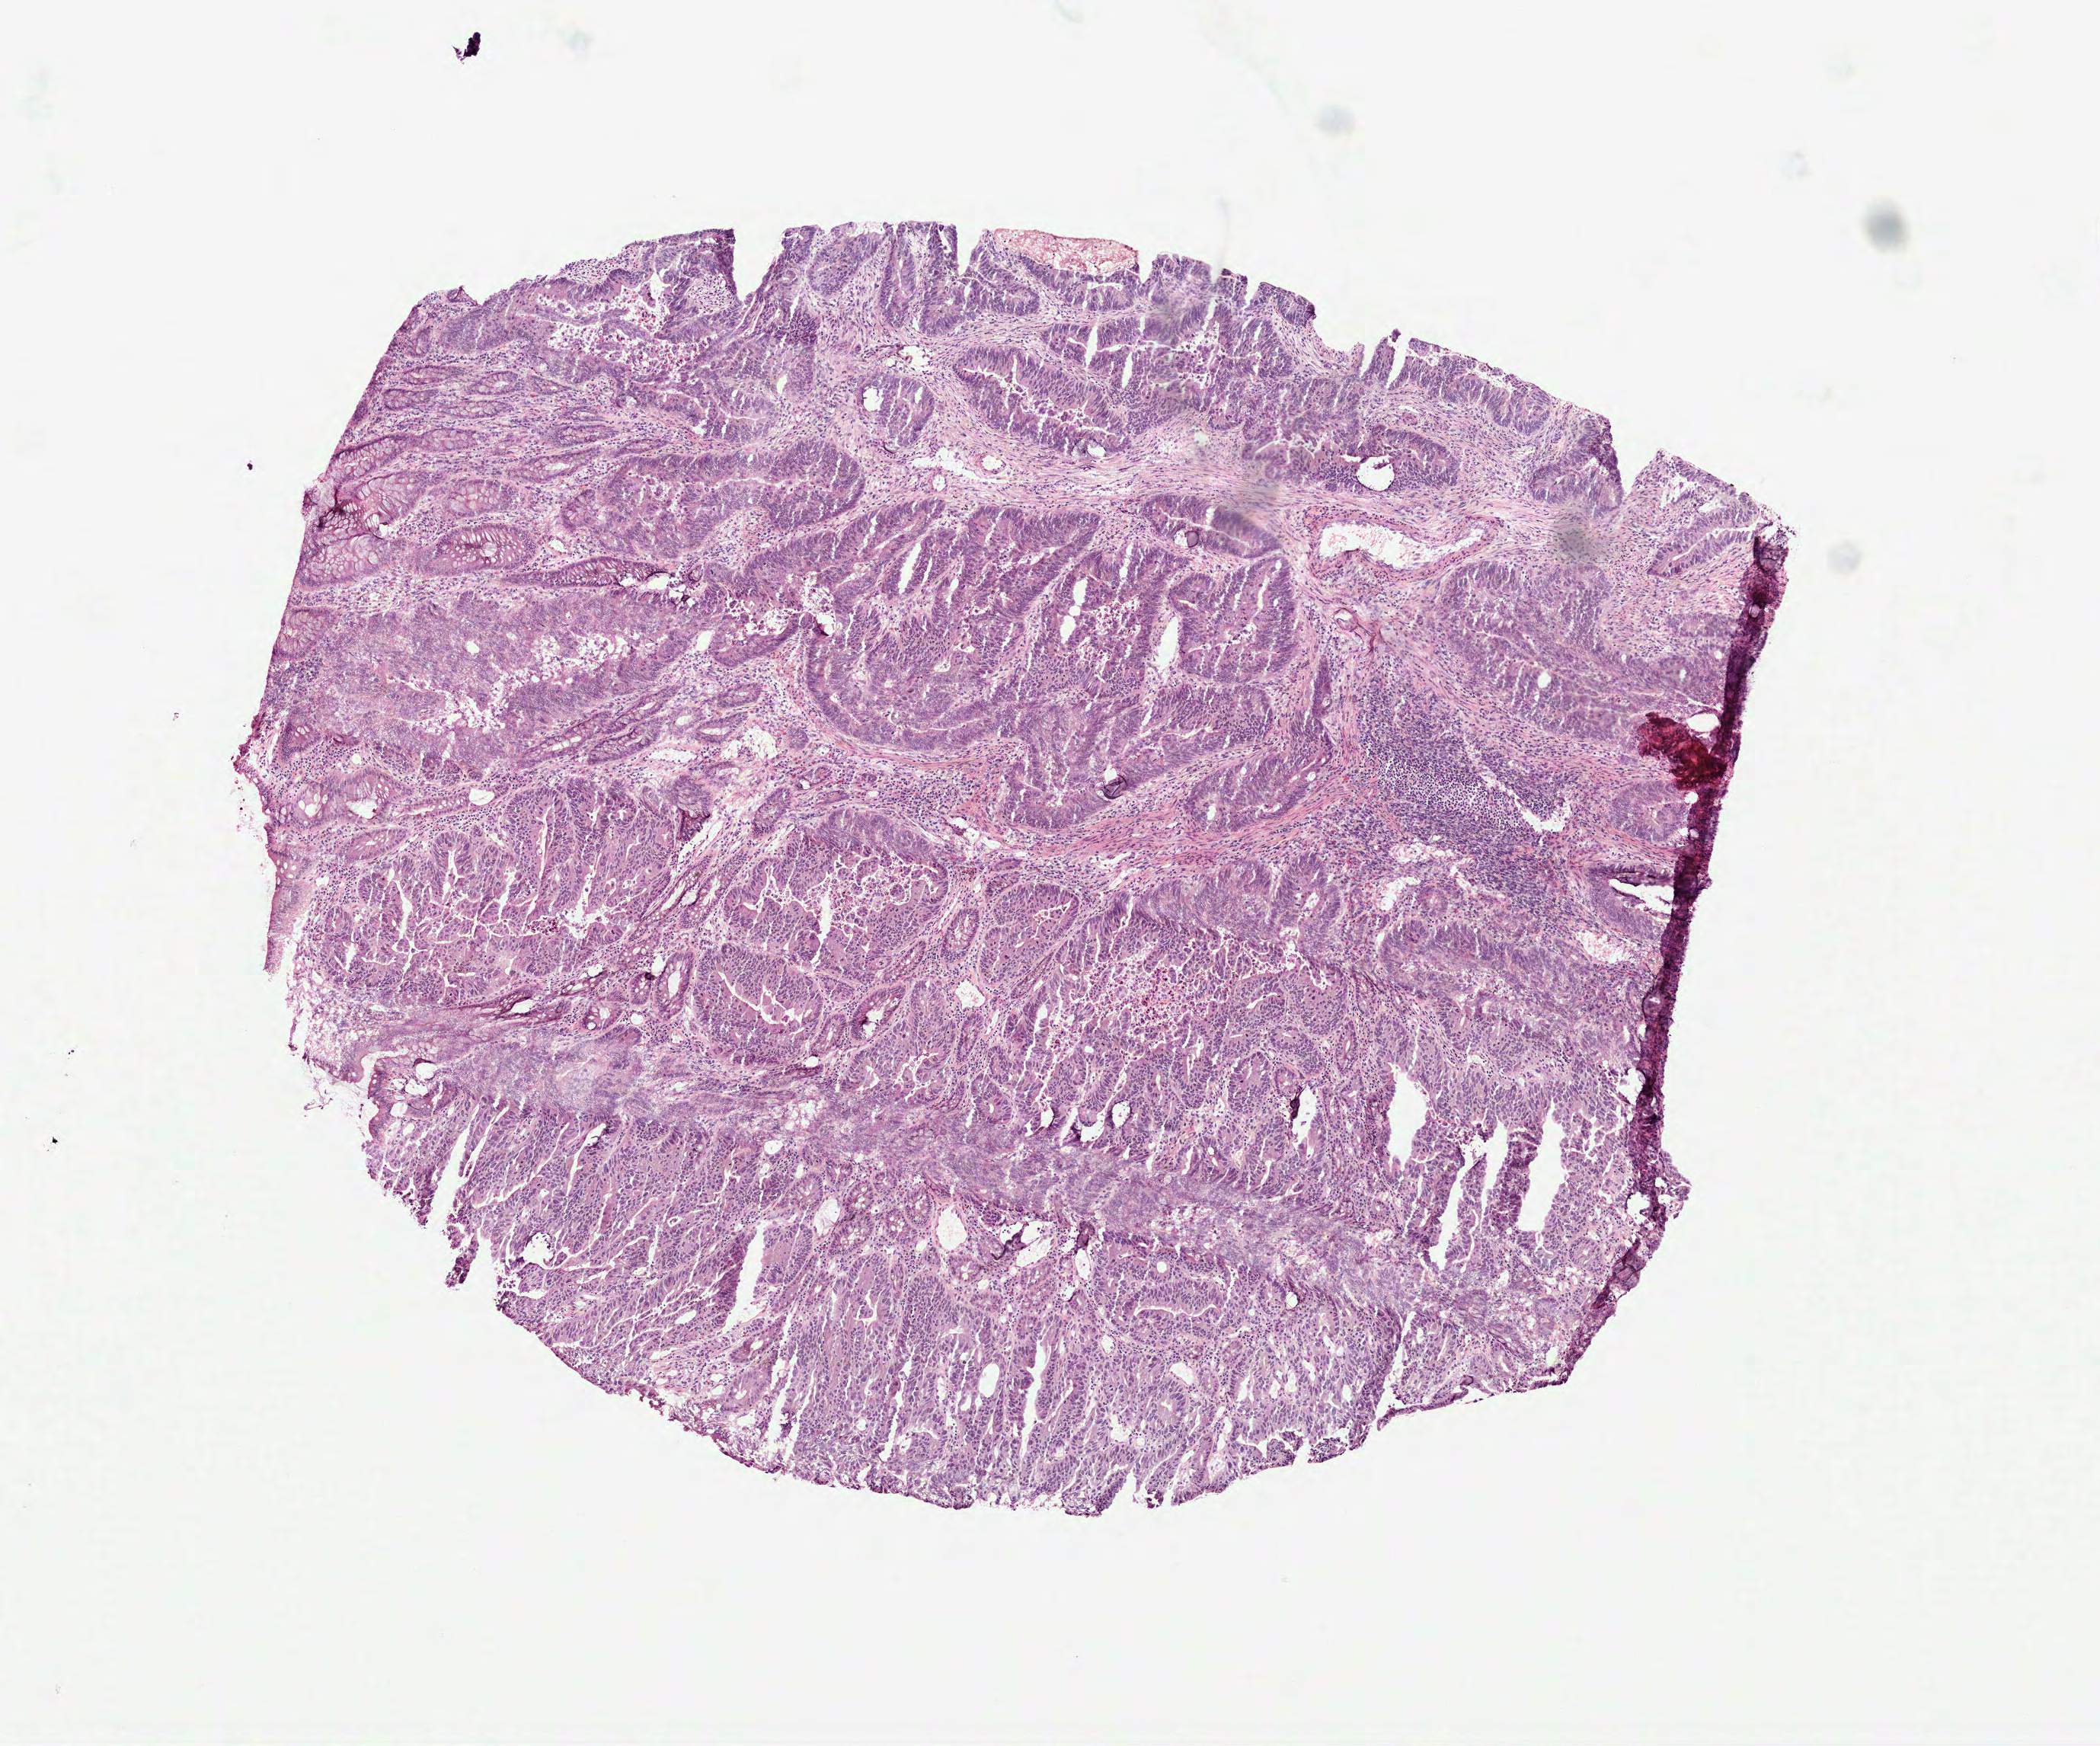
Whole-slide histology image, H&E — shown as a low-resolution overview of the whole scanned area (about 5.6 x 4.6 mm). Frozen section. Primary tumour sample from the colon. Female, age 45 years at initial diagnosis. Pathologist review of this section (percent, as recorded): tumour cells 99%, tumour nuclei 80%, normal cells 0%, stromal cells 0%, necrosis 1%. Inflammatory infiltration, as recorded: lymphocyte infiltration 10%, monocyte infiltration 2%, neutrophil infiltration 5%.
* lymph nodes positive (case pathology): 0 of 12 examined
* diagnosis: Adenocarcinoma, NOS